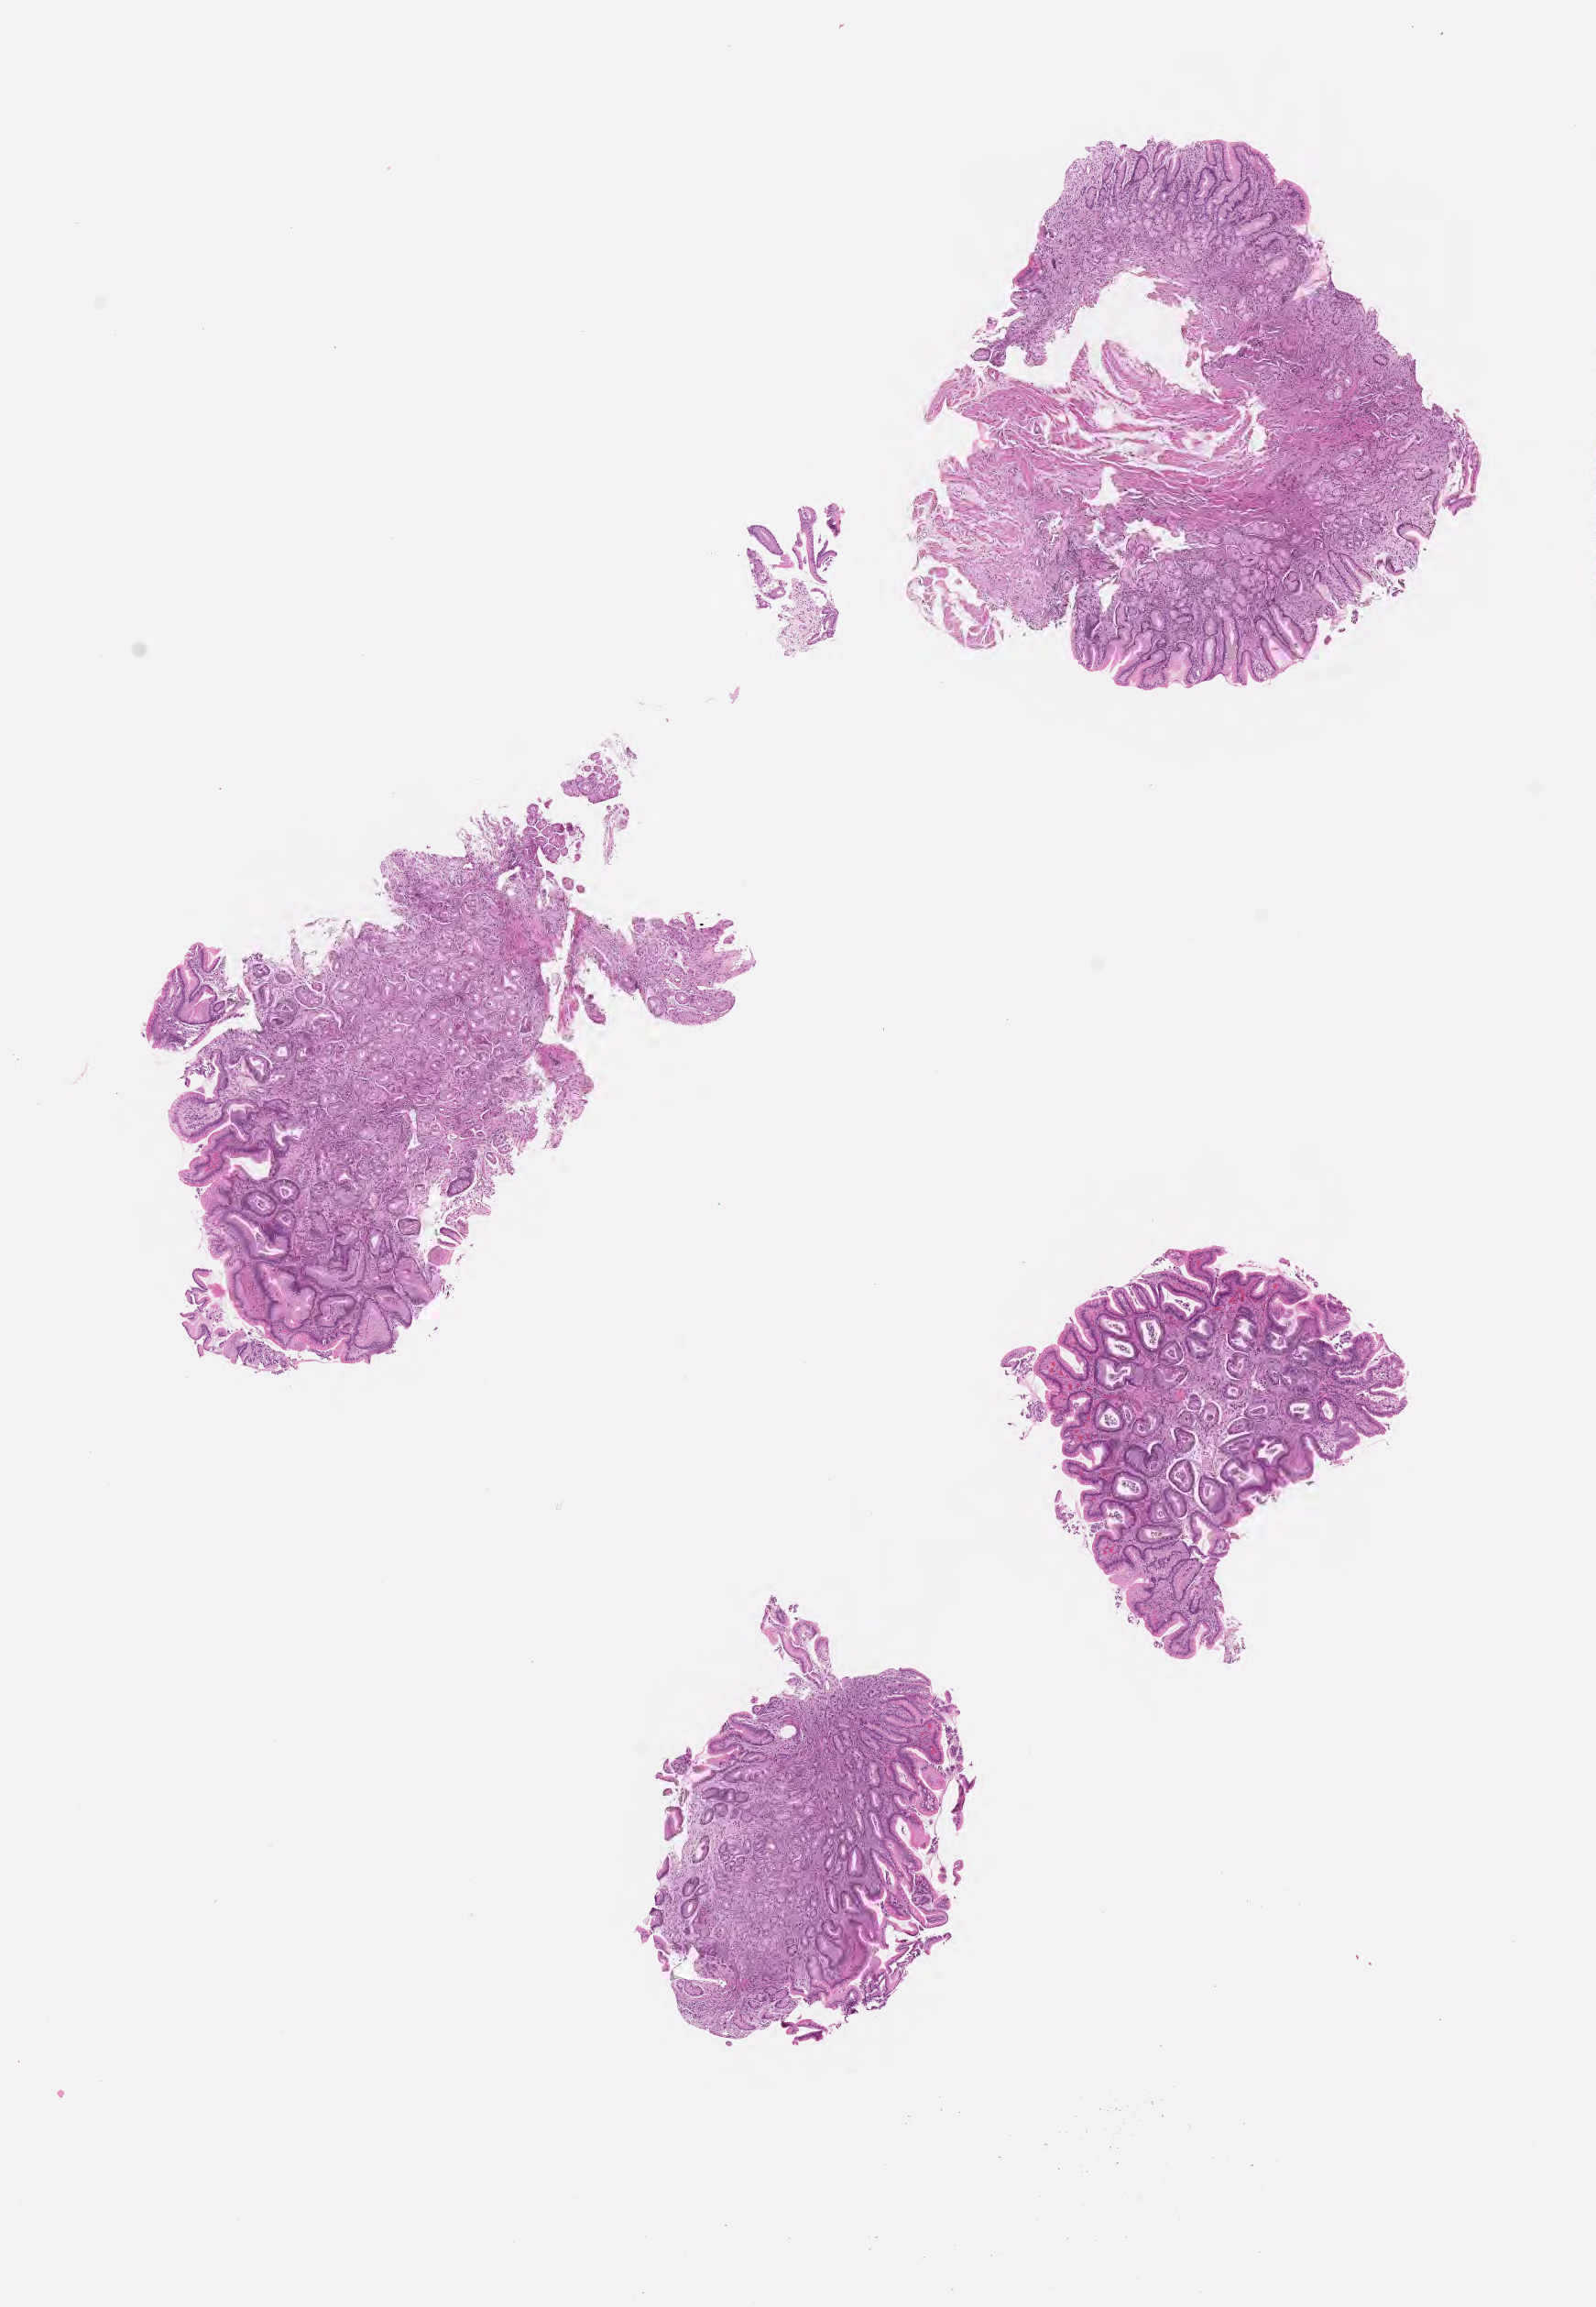
Whole-slide image, hematoxylin and eosin (H&E) stain — shown as a low-resolution overview of the whole scanned area (about 7.0 x 10.2 mm); formalin-fixed paraffin-embedded section; normal-tissue sample (non-tumor) from a patient with neoplasm, uncertain whether benign or malignant; anatomic site: bone marrow. Patient male; 70 years old. Pathologist review of this section (percent, as recorded): tumor cells 0%, tumor nuclei 0%, stromal cells 0%, necrosis 0%, normal cells 100%. Infiltration values recorded for this section: lymphocyte infiltration 80%, monocyte infiltration 10%, neutrophil infiltration 5%.
This section: non-tumor tissue sample; the patient's diagnosis is given above.